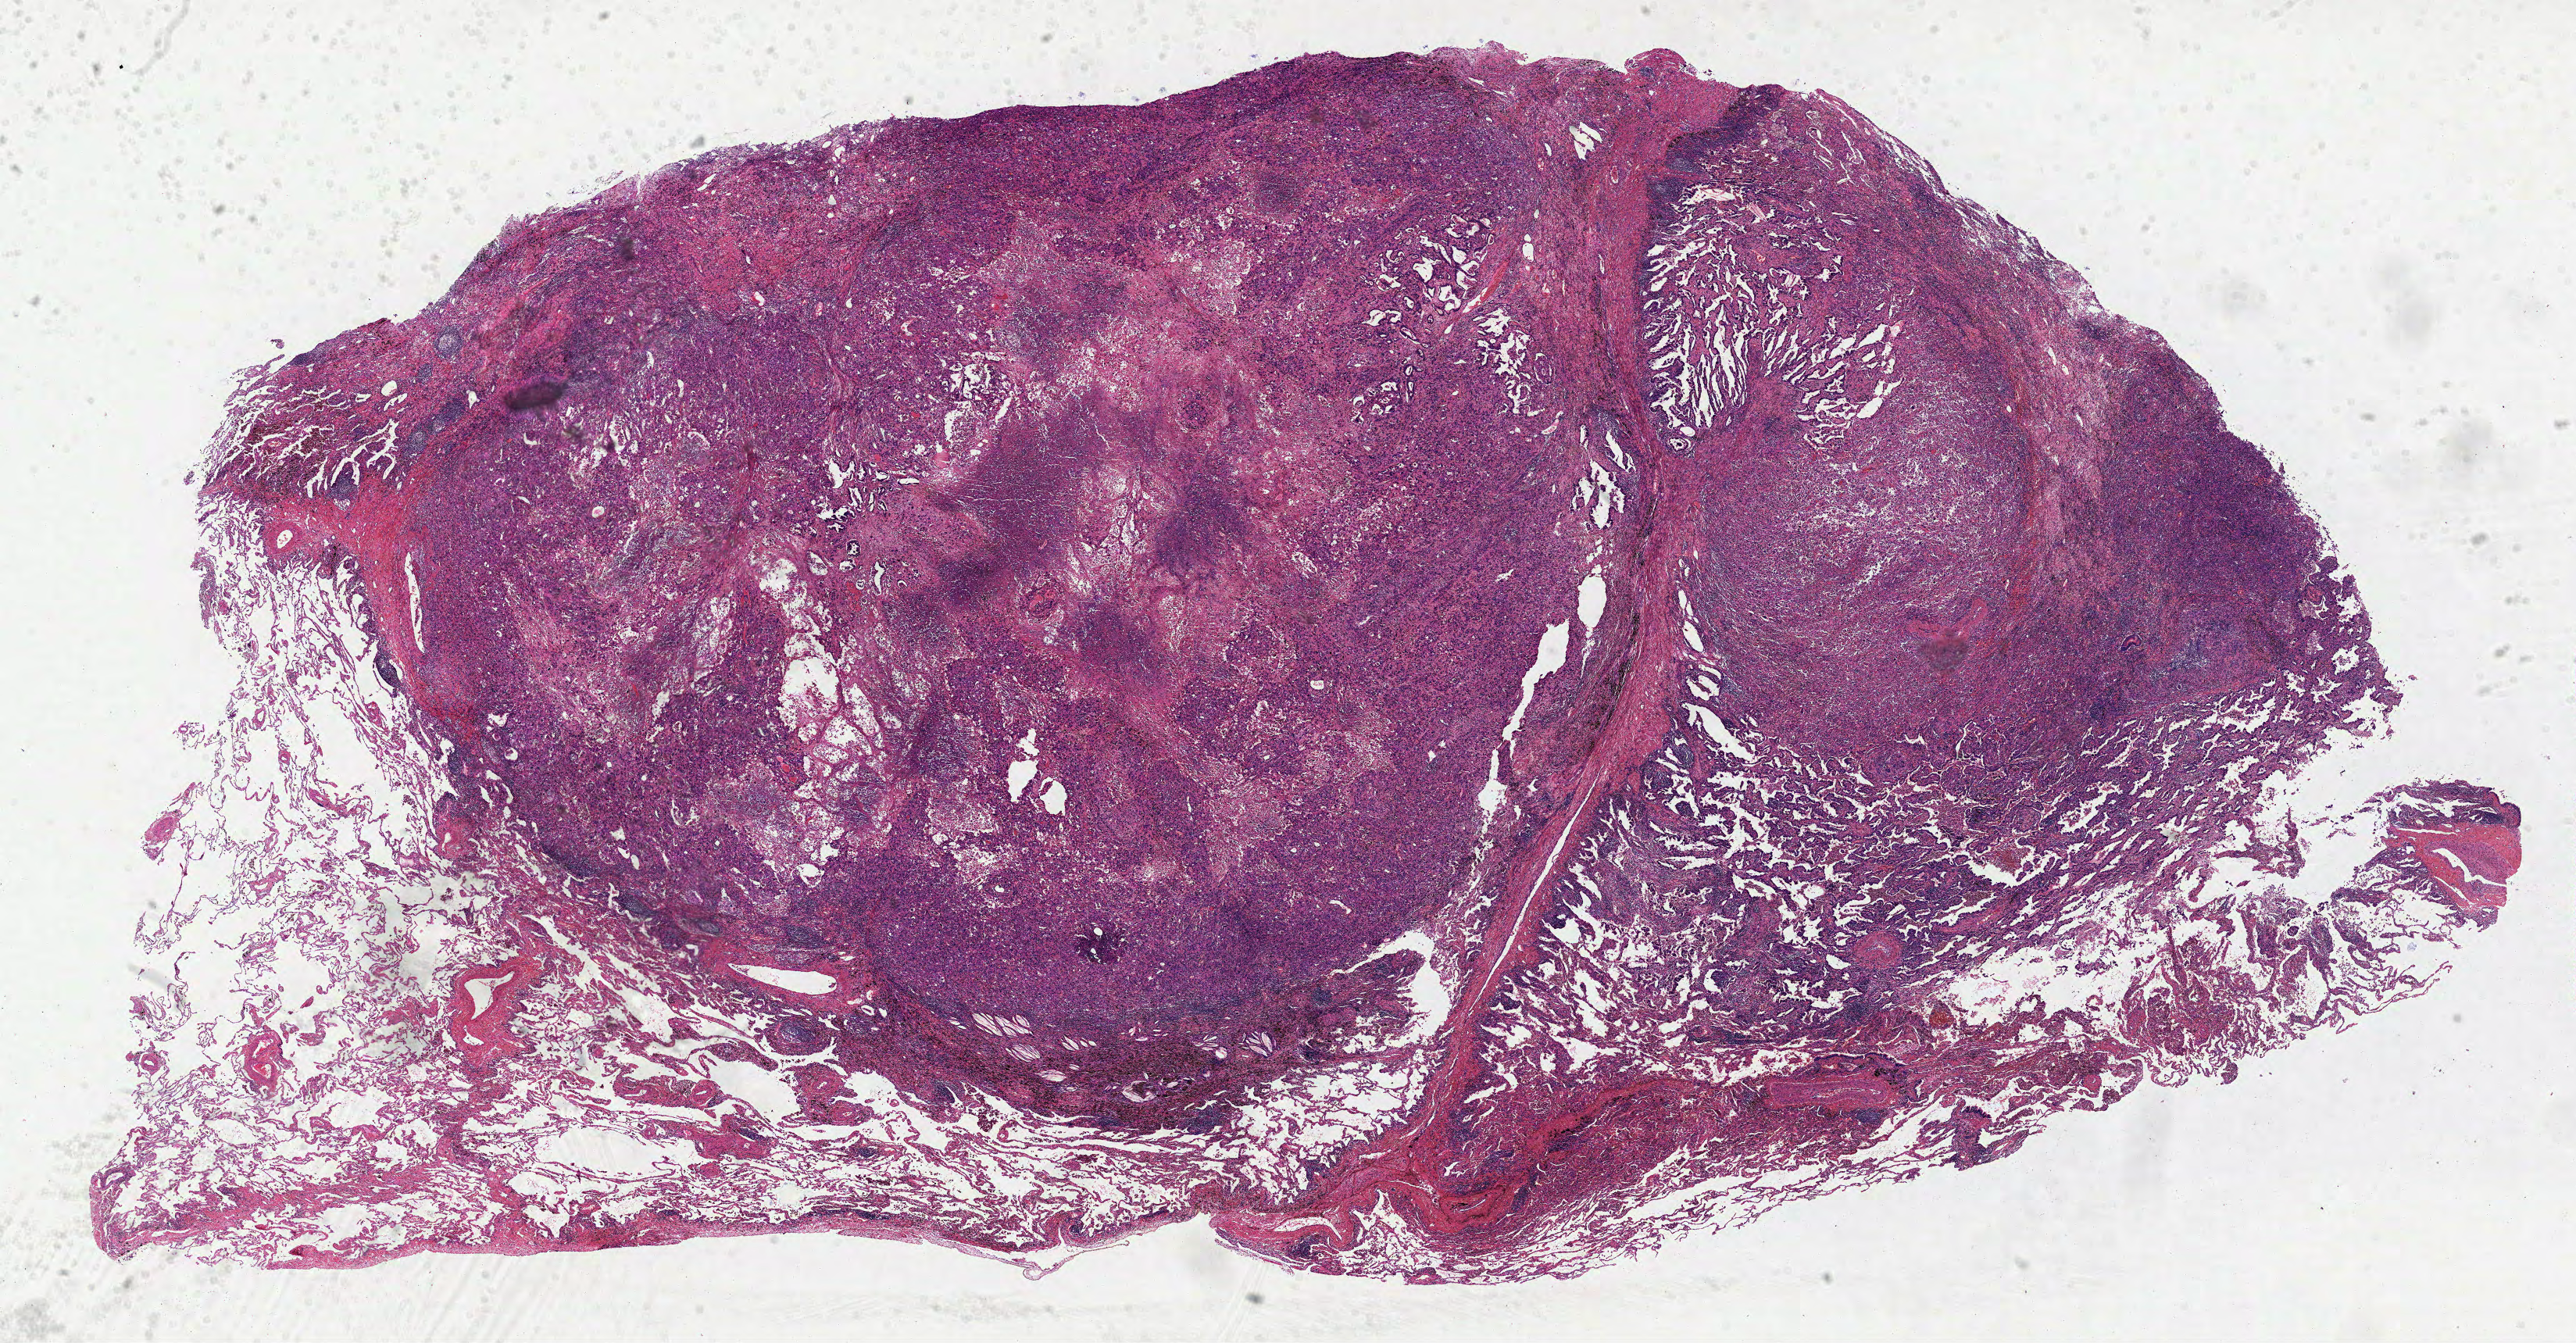
H&E-stained whole-slide image — whole scanned area (about 26.6 x 13.9 mm, acquisition: 40x scan) shown as a low-resolution overview, FFPE section, lung, primary tumour sample. Male, age 56 years at initial diagnosis.
Diagnosis: Adenocarcinoma, NOS.